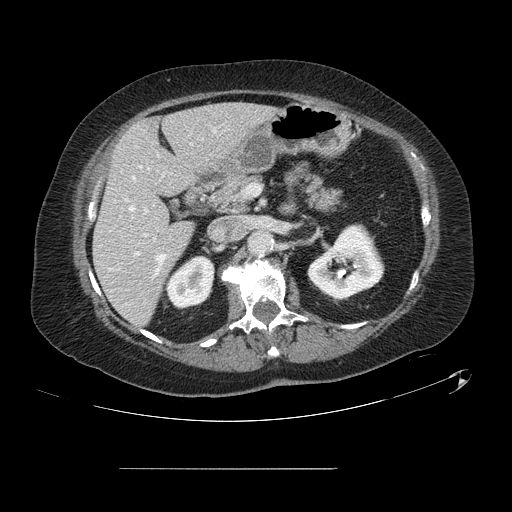
Contrast-enhanced abdominal CT, one axial slice. Slice 61 of 148 in the series (ordered by position). 120 kVp. Soft-tissue window (W 400 / L 40 HU). 2.5 mm slice thickness. 512 × 512 image matrix, field of view 439 × 439 mm. Female patient, age 75 years. From the clinical record (not read from this slice): diagnosis: colorectal cancer liver metastases, imaged before liver resection; multiple liver metastases: no; largest metastasis: 2.4 cm; disease in both lobes: no.
Outlined on this slice (manually delineated by an expert):
- hepatic veins: box from (x=126, y=177) to (x=165, y=274) px
- liver: (x=94, y=104)–(x=274, y=326)
- planned liver remnant (the part of the liver to remain after resection): (x=94, y=104)–(x=275, y=326)
- portal vein (with intrahepatic branches): (x=135, y=210)–(x=147, y=255)